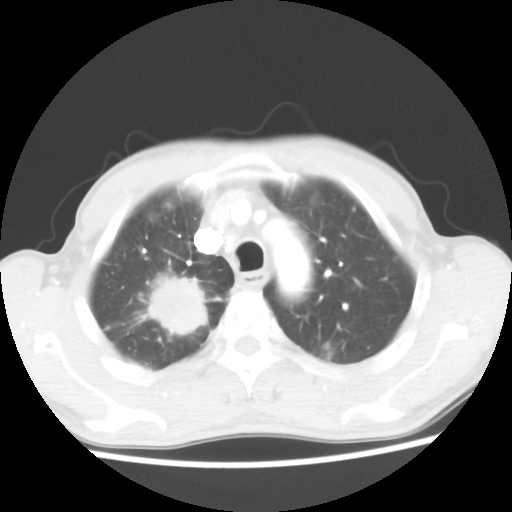
Chest CT, one axial slice; position 42 of 52 along the scan axis; lung window (W 1500 / L -600 HU); 5 mm slice thickness; 512 × 512 image matrix, field of view 323 × 323 mm. Male patient, age 66 years. From the clinical record (not read from this slice): clinical TNM (as recorded): T2 N0 M1a.
Annotated regions visible in this slice (rectangle marked by the reading radiologist):
- lung tumour (recorded histology: adenocarcinoma): bounding box <130,266,217,337> (left, top, right, bottom; pixels)